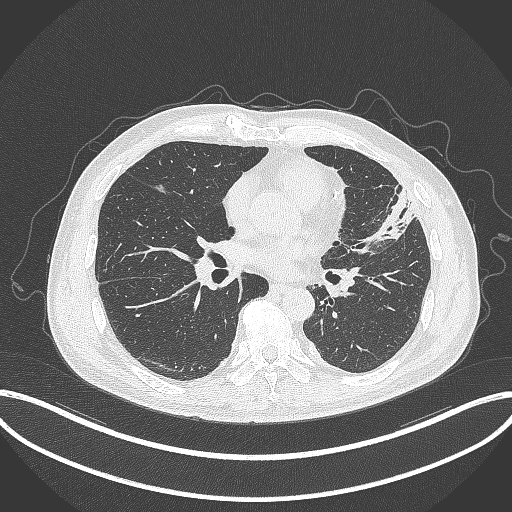
Chest CT, one axial slice; reconstruction kernel B70f; 120 kVp; lung window (W 1500 / L -600 HU); 1 mm slice thickness; 512 × 512 image matrix, field of view 415 × 415 mm. Patient: male, 64 years. Case-level facts recorded for this patient, not image findings: clinical TNM (as recorded): T4 N1 M0; histopathological grade: G3.
Structures marked on this image (rectangle marked by the reading radiologist):
- lung tumour (recorded histology: adenocarcinoma): box from (x=359, y=183) to (x=420, y=245) px